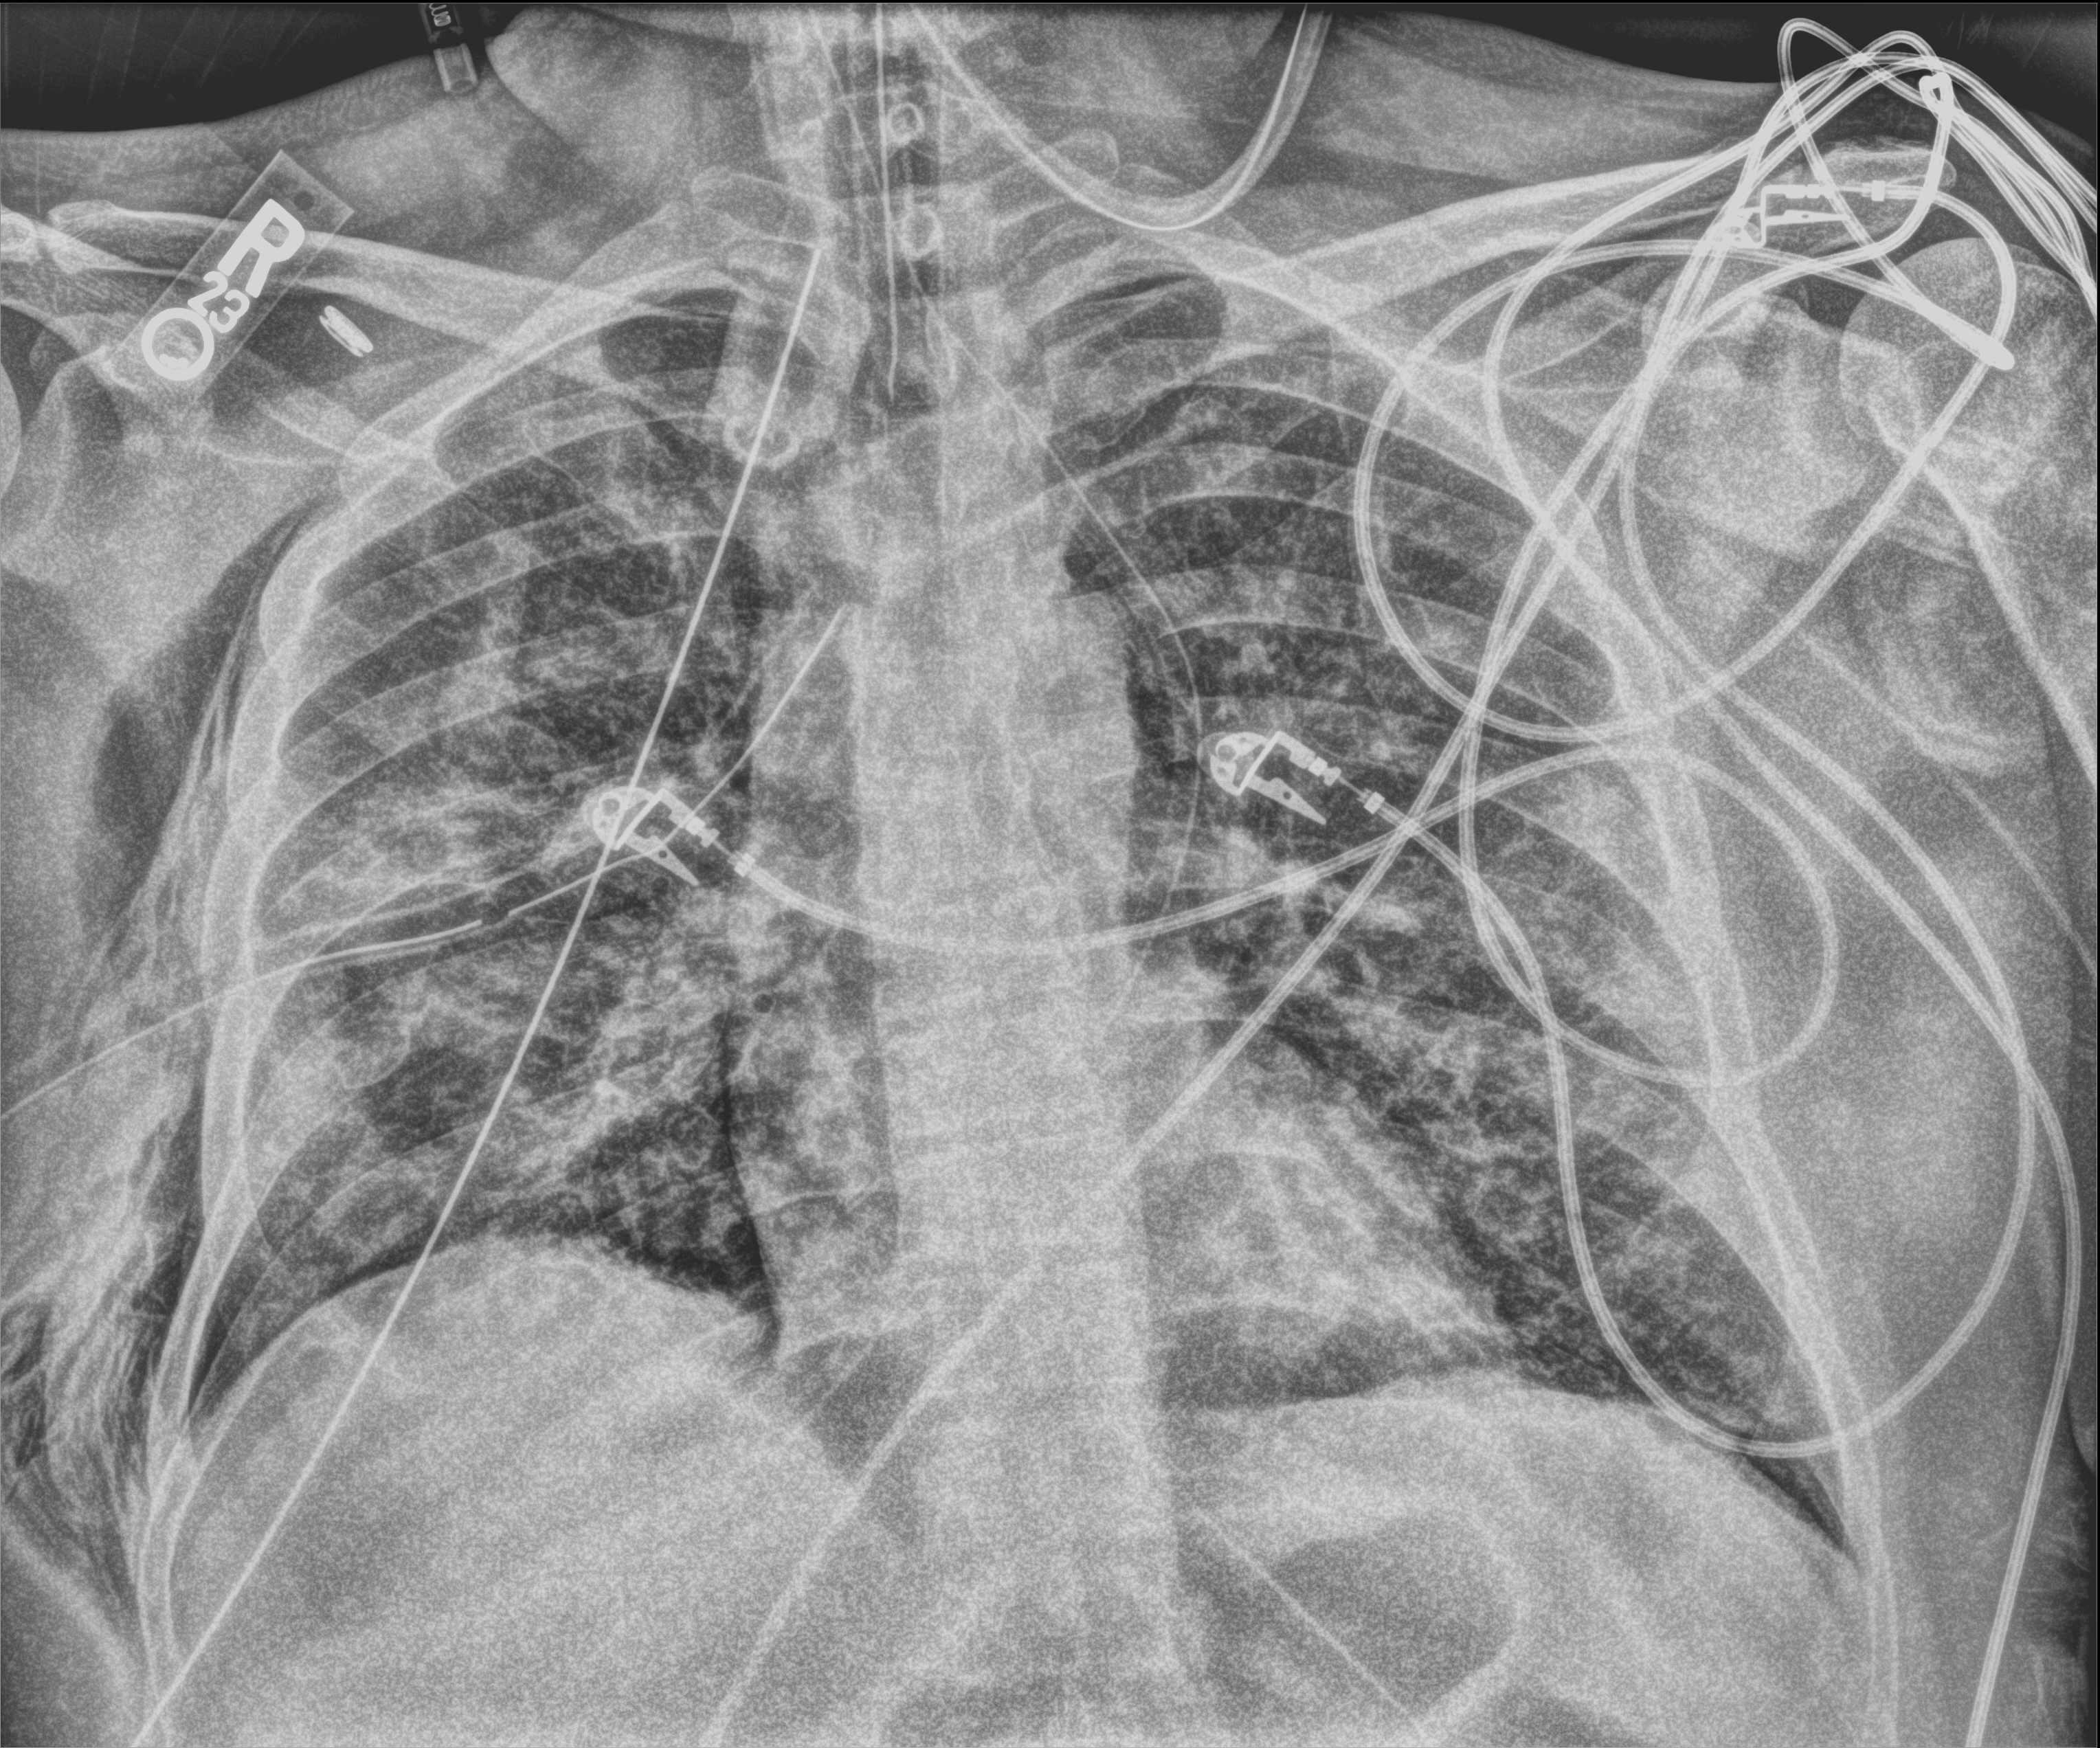
Bedside chest radiograph (computed radiography); anteroposterior (AP) projection. Male patient hospitalised with COVID-19, age 18–59 years.
Admission-level facts for this patient (not findings on this image; timing relative to this image not recorded): mechanically ventilated during this hospital stay: yes; admitted to intensive care during this hospital stay: yes.